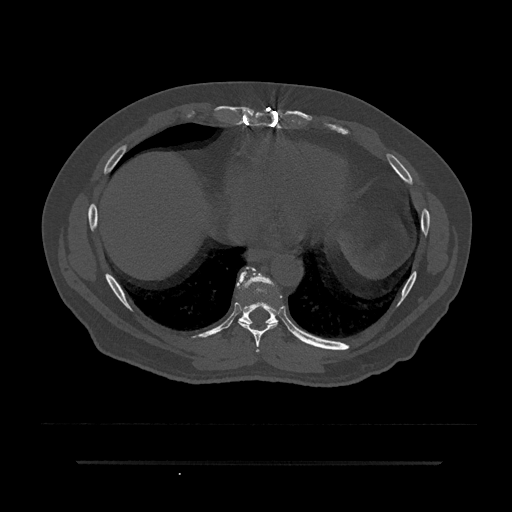
CT including the spine, one axial slice. Slice 404 of 797 in the series (ordered by position). 120 kVp. Bone window (W 1800 / L 400 HU). 0.5 mm slice thickness. 512 × 512 image matrix. Male patient, age 59 years. From the clinical record (not read from this slice): primary cancer: bile ducts.
Annotated regions visible in this slice (semi-automatic segmentation, software-assisted and operator-edited):
- T7 vertebra: bounding box [x1, y1, x2, y2] px = [256, 349, 259, 352]
- T8 vertebra: [238, 267, 278, 352]
- T9 vertebra: [236, 267, 280, 326]